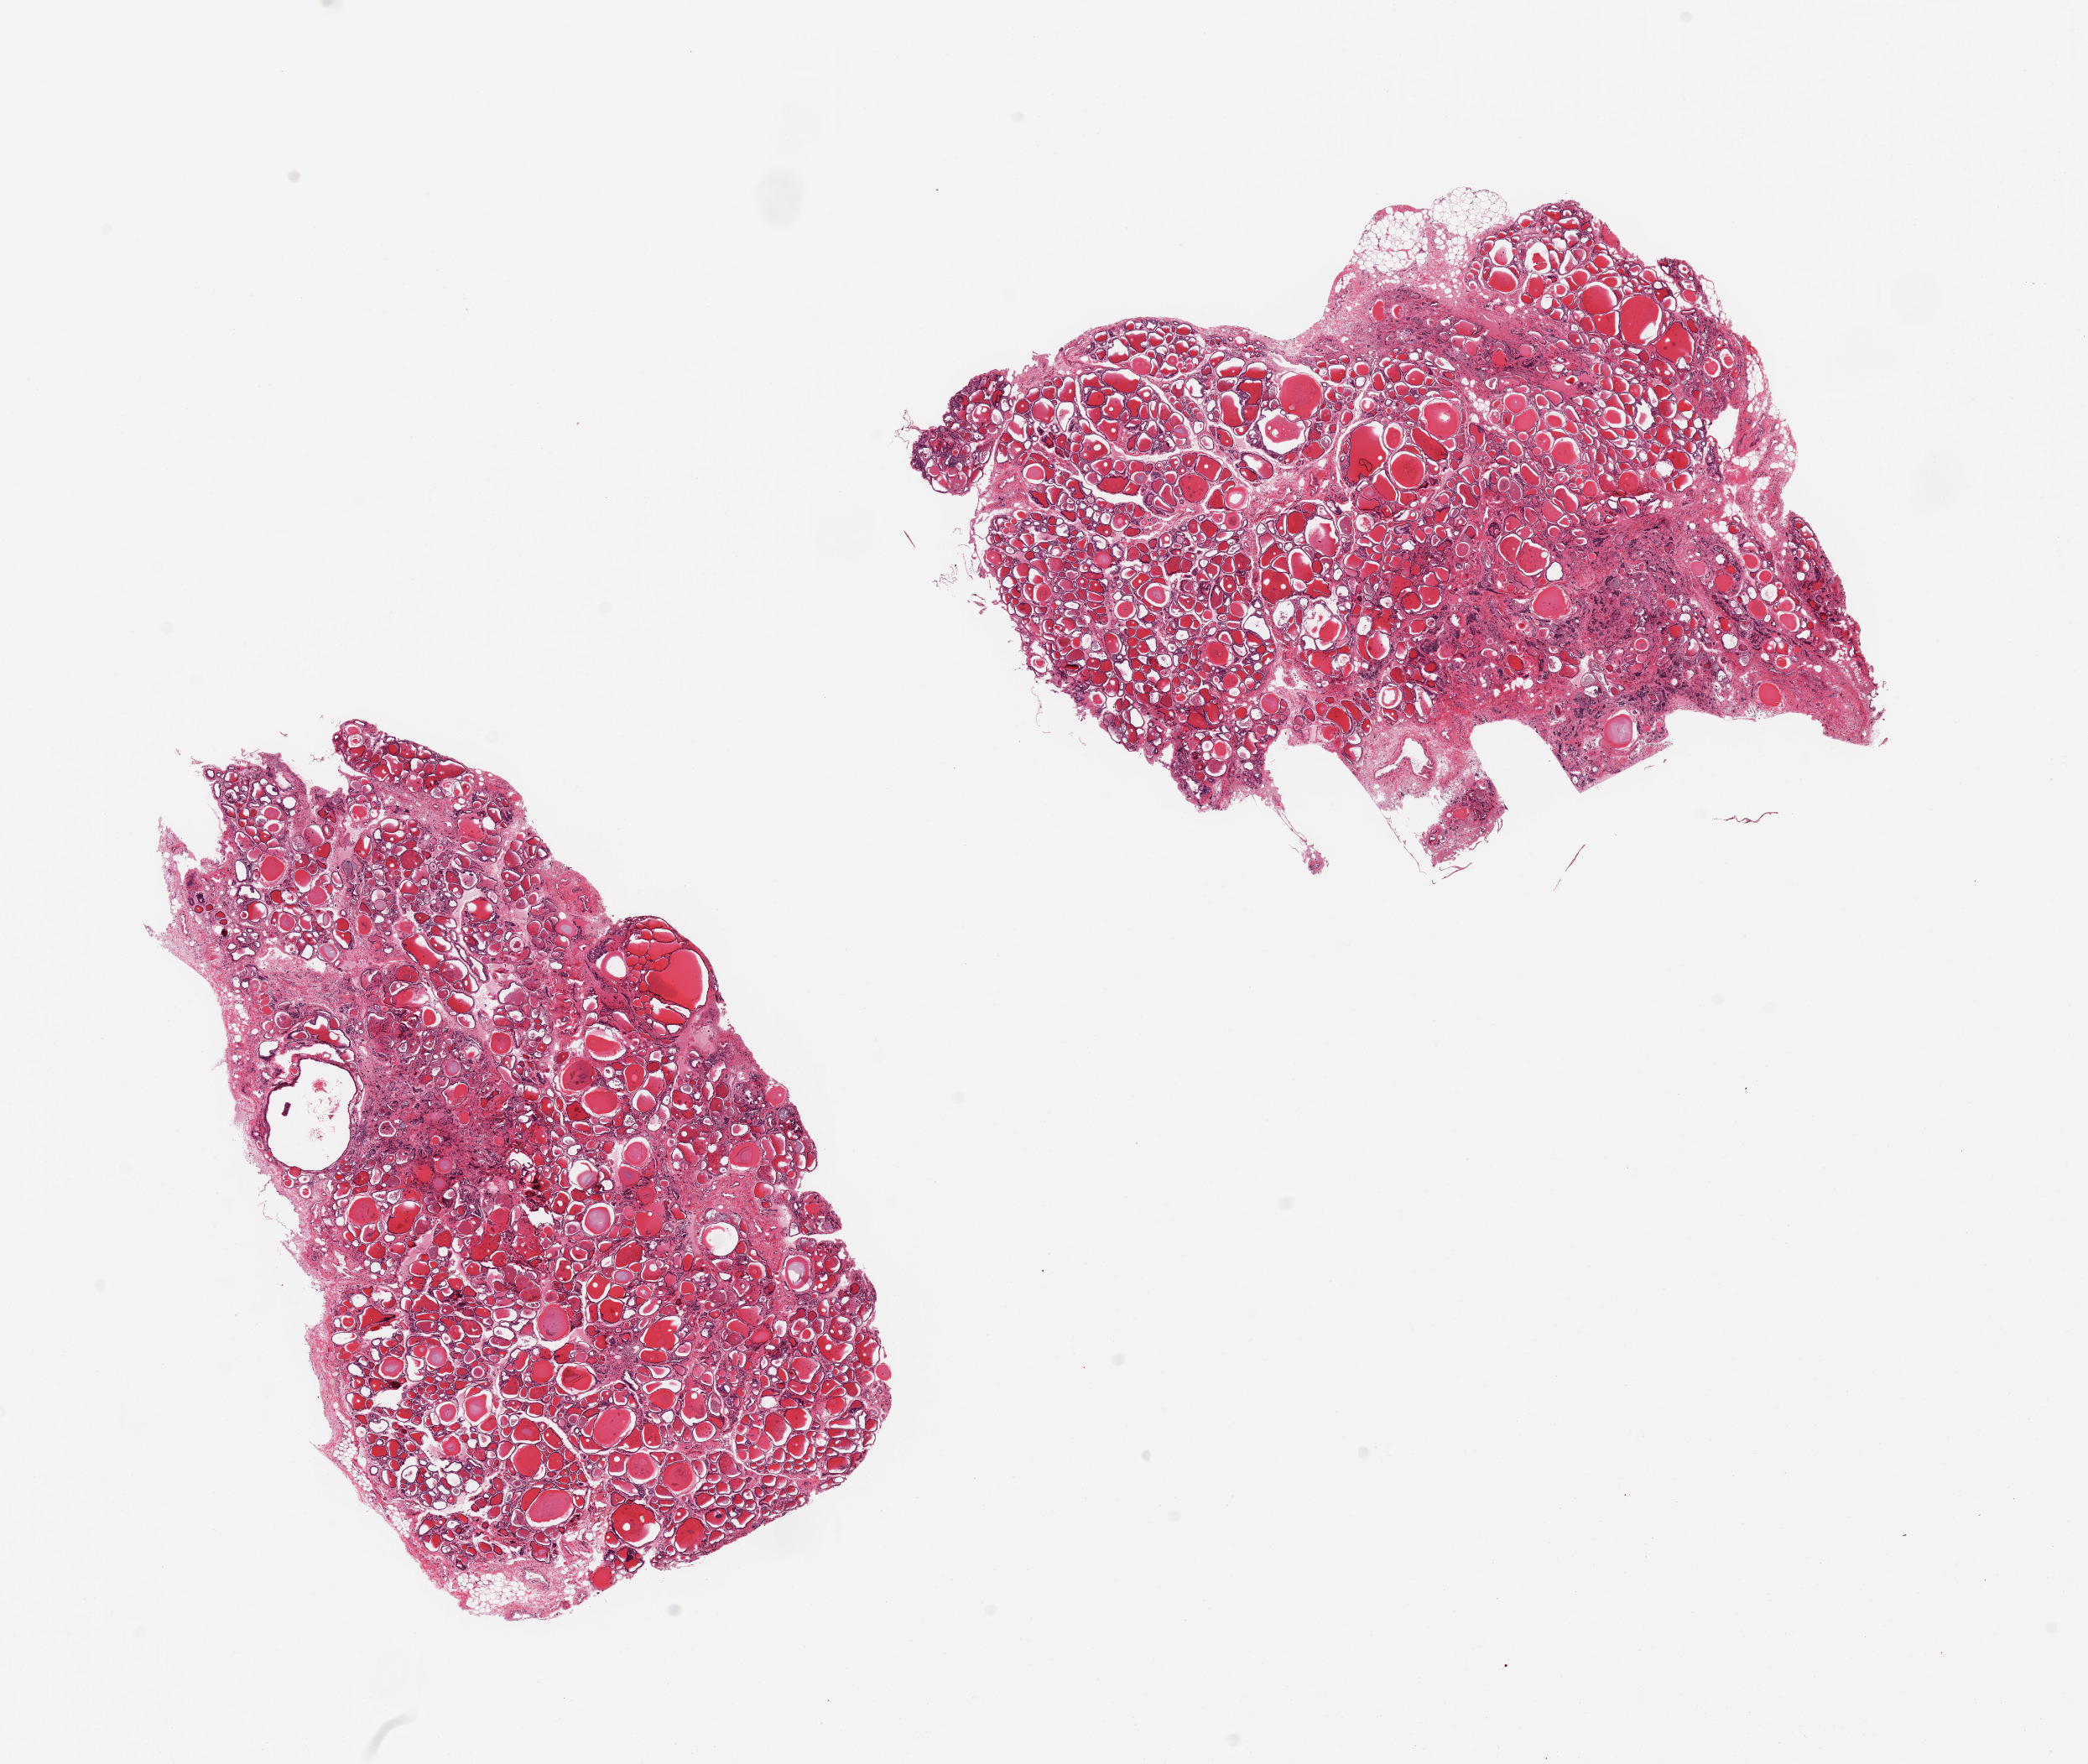
Whole-slide image, hematoxylin and eosin (H&E) stain — a low-resolution overview of the entire scanned area, about 19.7 x 16.6 mm (acquisition: 20x scan). PAXgene-fixed paraffin-embedded (PFPE) section. Target tissue: thyroid. Tissue donor sample. Donor: female.
Pathologist's review note for this sample: 2 pieces; focal atrophy.